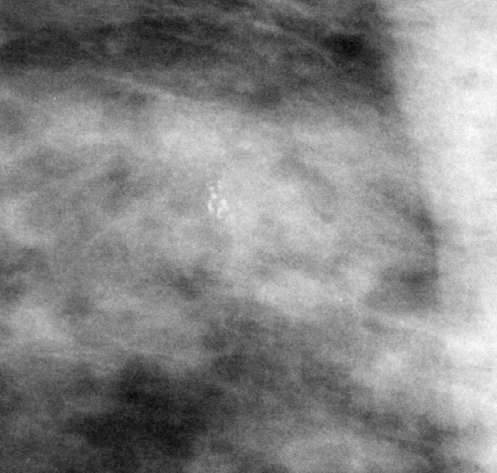
Region of interest cut from a scanned film mammogram (one marked finding); right breast; MLO view.
Calcifications, morphology amorphous, distribution clustered; BI-RADS assessment category 4; subtlety rating 2 on a 1 (subtle) to 5 (obvious) scale; pathology (as recorded): benign.